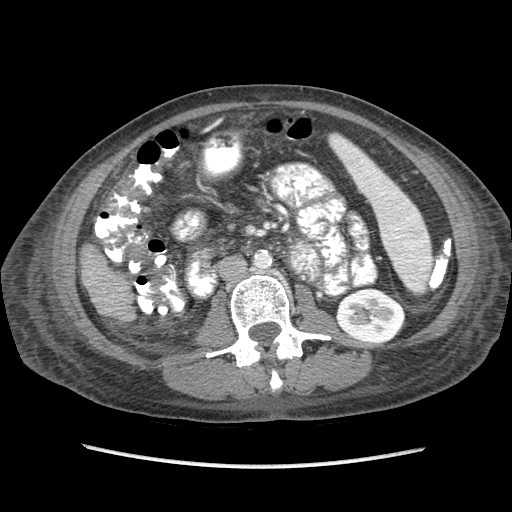
Contrast-enhanced abdominal CT (liver protocol), one axial slice. Slice 19 of 87 in the series (ordered by position). Reconstruction kernel STANDARD. 120 kVp. Soft-tissue window (W 400 / L 40 HU). 512 × 512 image matrix, field of view 340 × 340 mm. Case-level facts recorded for this patient, not image findings: diagnosis: hepatocellular carcinoma (patient treated with transarterial chemoembolisation; whether this scan precedes or follows treatment is not stated here); TNM stage (as recorded): Stage-IIIB.
Outlined on this slice (semi-automatically segmented with operator editing):
- liver parenchyma outside the tumour (the mass and vessels are separate outlines, so this box may not span the whole liver): box from (x=80, y=244) to (x=132, y=315) px